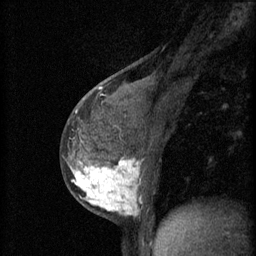
Breast MRI (dynamic contrast-enhanced), one sagittal slice; position 28 of 60 along the scan axis; 3 images stored at this slice position (order not interpretable as contrast timing); 1.5 T; TE 4.2 ms, TR 11 ms; 2 mm slice thickness; 256 × 256 image matrix, field of view 180 × 180 mm. Patient: female, 37 years.
Outlined on this slice (semi-automatically segmented with operator editing):
- analysis volume of interest (the breast-tissue region the enhancement analysis was run in; not a lesion): bounding box (x1, y1, x2, y2) in pixels: (65, 138, 174, 221)
- tumour enhancement mask (voxels above the 70 % enhancement threshold inside the analysis volume of interest): (71, 160, 141, 215)